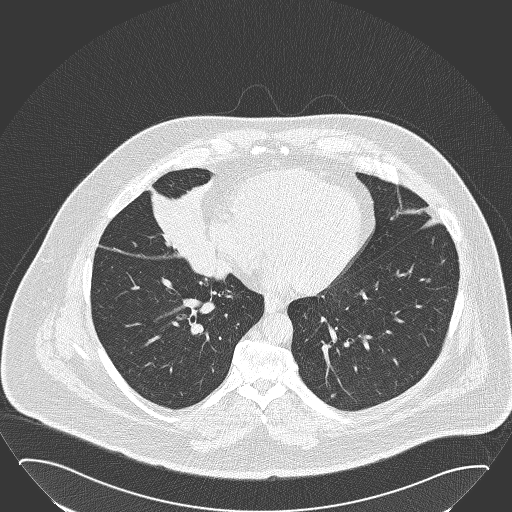
Axial slice from a low-dose chest CT screening exam. Baseline annual screen. Lung window (W 1500 / L -600 HU). 512 × 512 image matrix. Male, age 61 years at enrolment.
- Lesion marked by an expert reader, bounding box [x1, y1, x2, y2] px = [134, 174, 227, 263].
- The screening reader recorded 2 non-calcified nodules or masses ≥4 mm on this exam; which of them this box marks is not recorded.
- Official screen result: positive, change unspecified: nodule(s) >= 4 mm or enlarging nodule(s), mass(es), or other non-specific abnormalities suspicious for lung cancer.
- Participant outcome: lung cancer diagnosed 47 days after this screen — basaloid squamous cell carcinoma, right middle lobe, right hilum, poorly differentiated (G3), stage IIB (AJCC 6th edition), 95 mm at pathology.